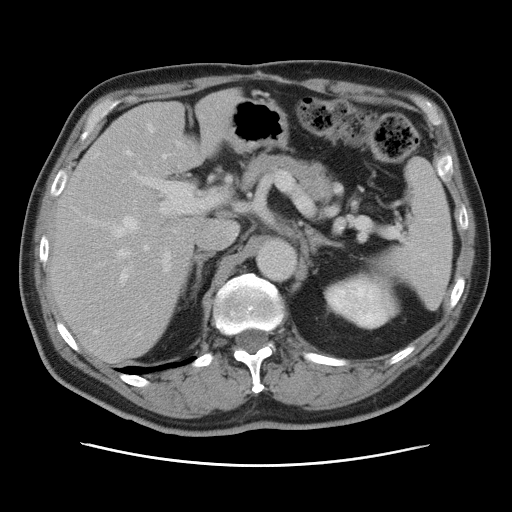
Contrast-enhanced abdominal CT, one axial slice. Position 49 of 80 along the scan axis. Intravenous contrast given. Soft-tissue window (W 400 / L 40 HU). 5 mm slice thickness. 512 × 512 image matrix. Male patient, age 69 years. From the clinical record (not read from this slice): diagnosis: colorectal cancer liver metastases, imaged before liver resection; multiple liver metastases: no; largest metastasis: 5 cm; disease in both lobes: yes.
Structures marked on this image (outlined manually by an expert reader):
- hepatic veins: bounding box [x1, y1, x2, y2] px = [94, 125, 169, 337]
- liver: [50, 92, 238, 361]
- planned liver remnant (the part of the liver to remain after resection): [50, 92, 238, 361]
- portal vein (with intrahepatic branches): [116, 143, 205, 273]